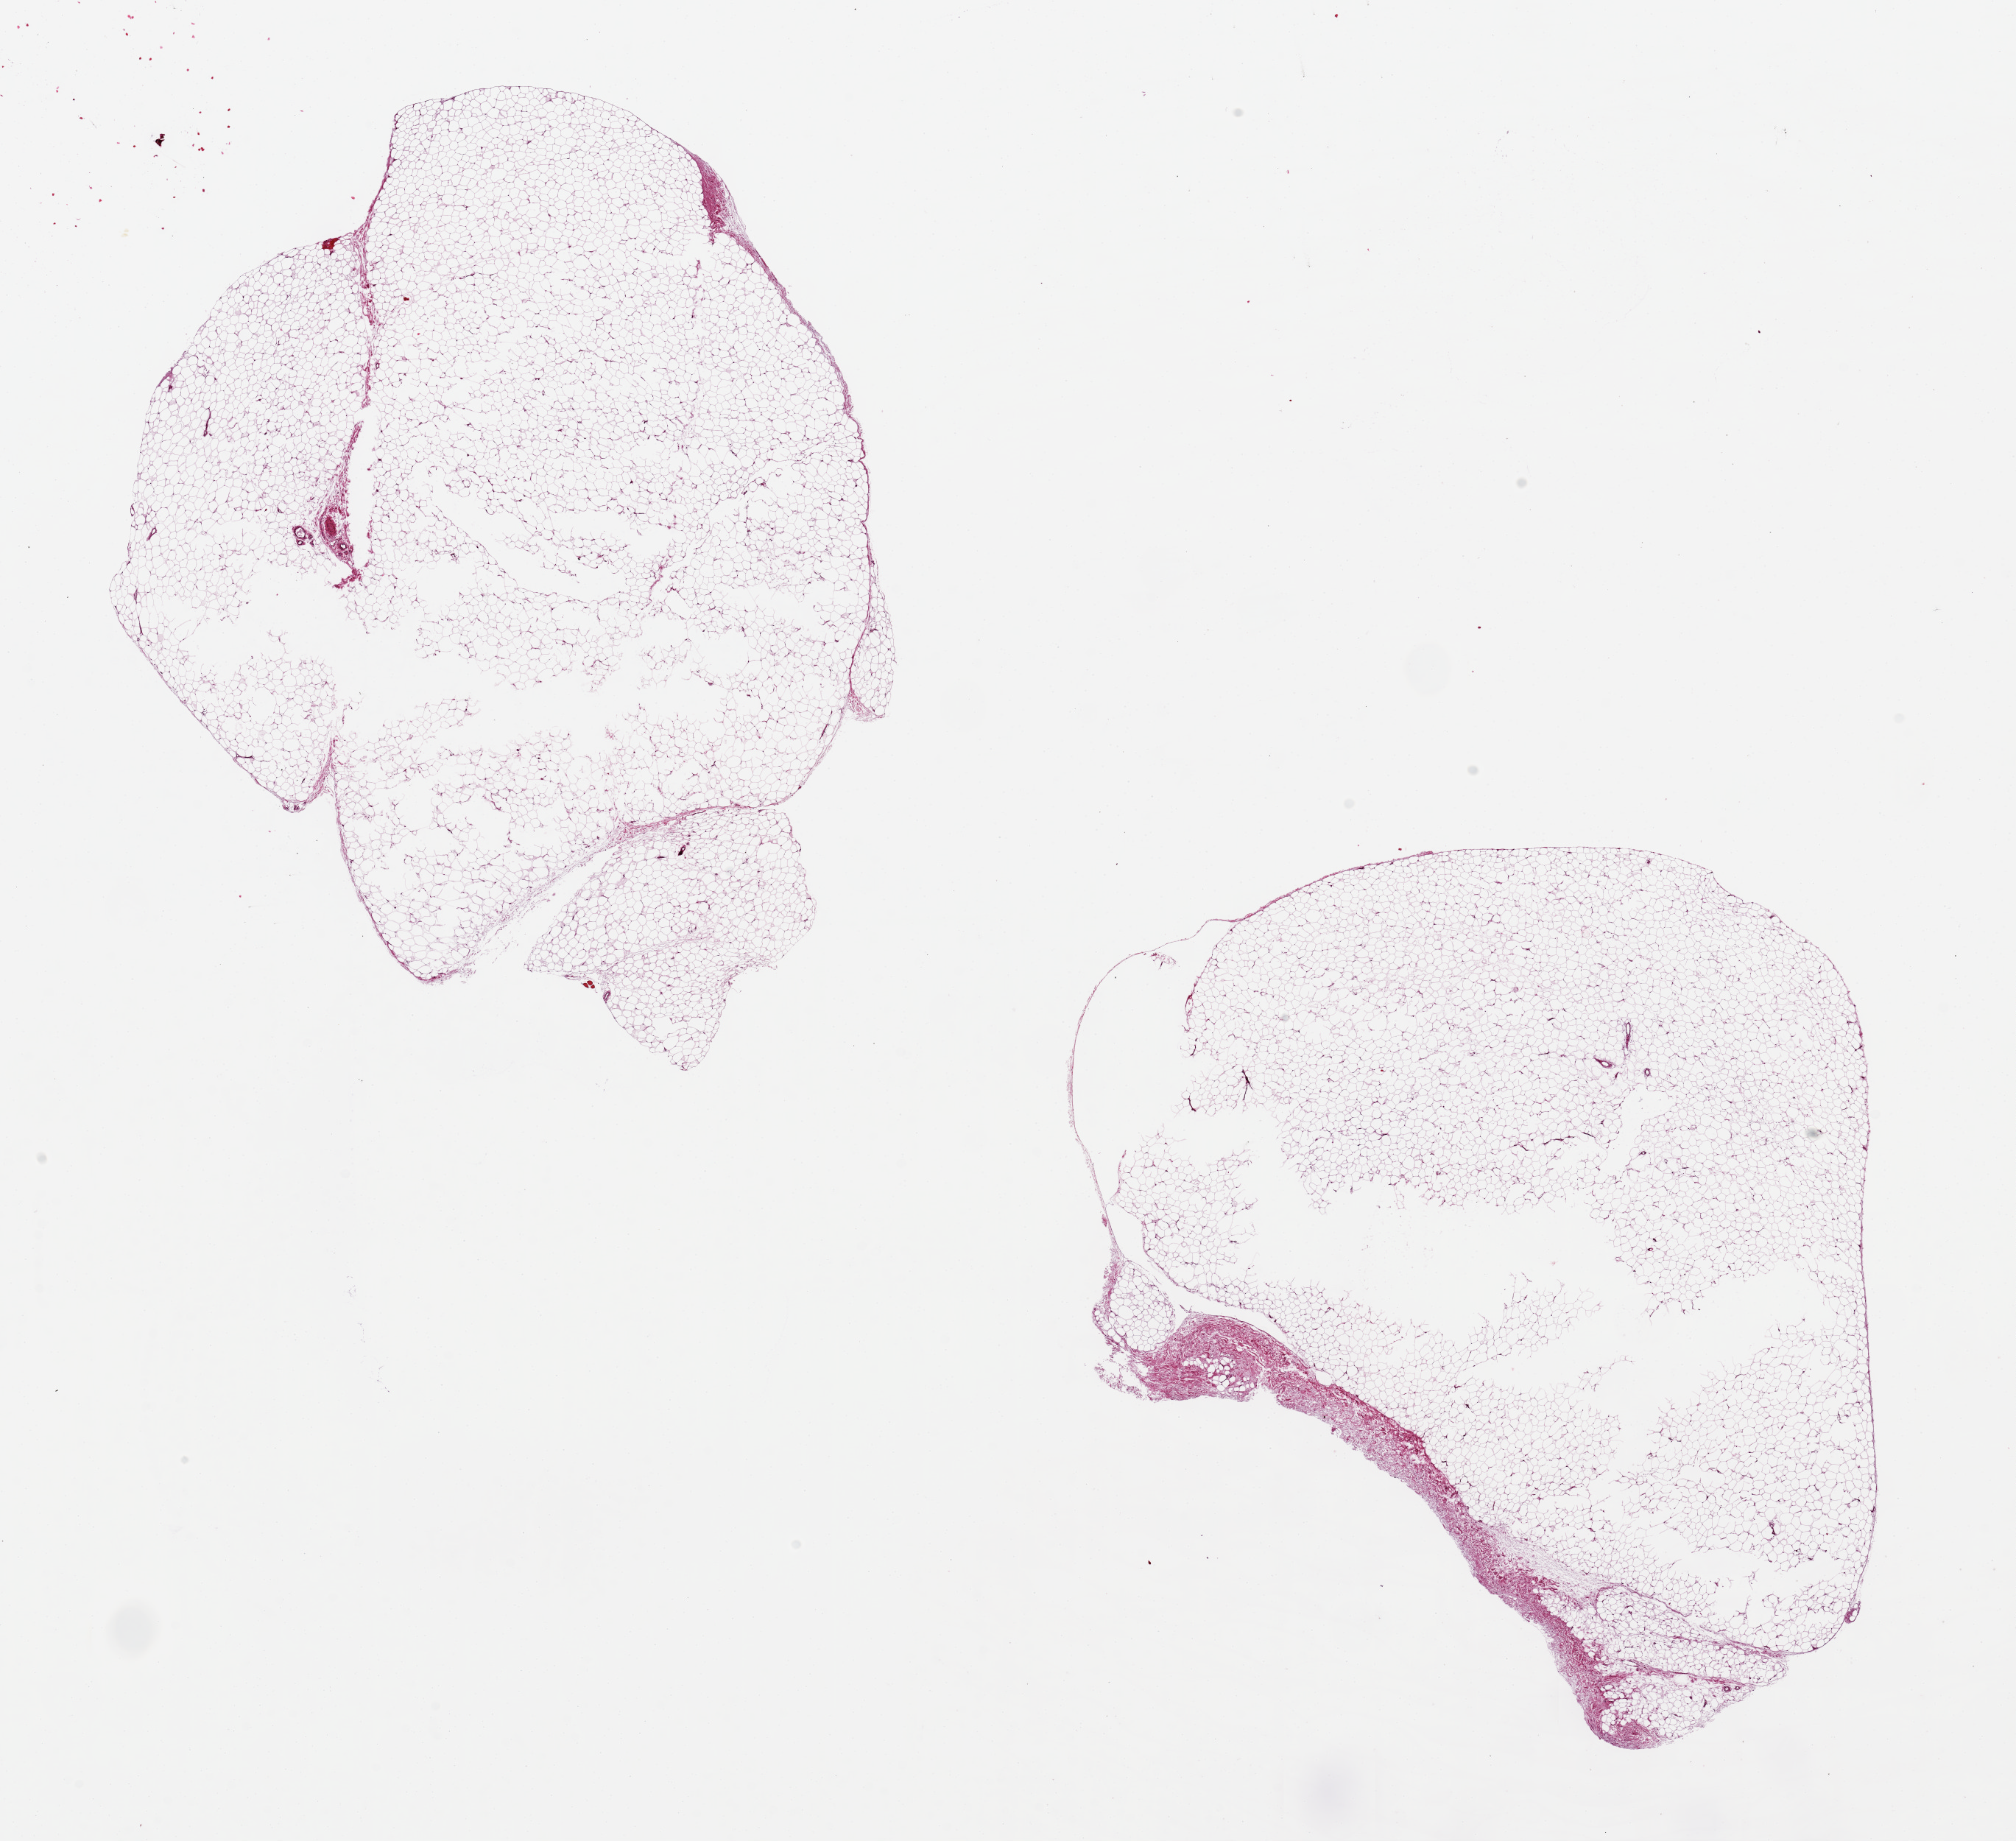
Digitized hematoxylin and eosin (H&E)-stained section — shown as a low-resolution overview of the whole scanned area (about 21.7 x 19.8 mm). PAXgene-fixed paraffin-embedded (PFPE) section. Section of adipose tissue (target tissue). Donor tissue sample. Donor: female.
• reviewer comment on this tissue sample: 2 aliquots, ~9x7mm